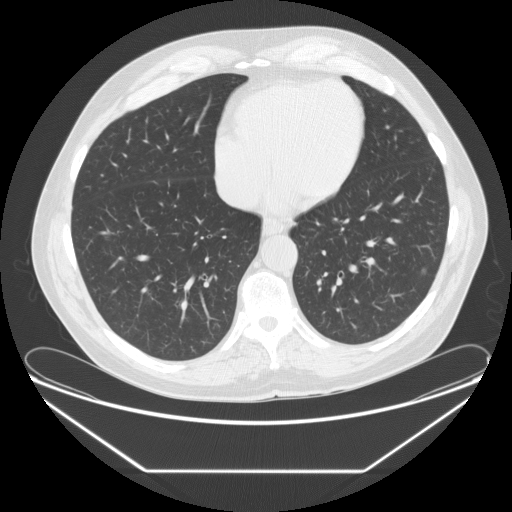
Axial slice from a low-dose chest CT screening exam, baseline screening round, lung window (W 1500 / L -600 HU), standard (soft-tissue) reconstruction kernel (STANDARD), 120 kVp, slice 171 of 261 in the series, 512 × 512 image matrix. Male, age 67 years at enrolment. Current smoker at enrolment.
Expert reader's lesion annotation, box from (x=413, y=259) to (x=435, y=283) px. The exam's reader record, not a measurement of the box and not confirmed to be the same lesion: non-calcified nodule or mass ≥4 mm, left lower lobe, 4 × 4 mm, poorly defined margins, soft tissue attenuation.